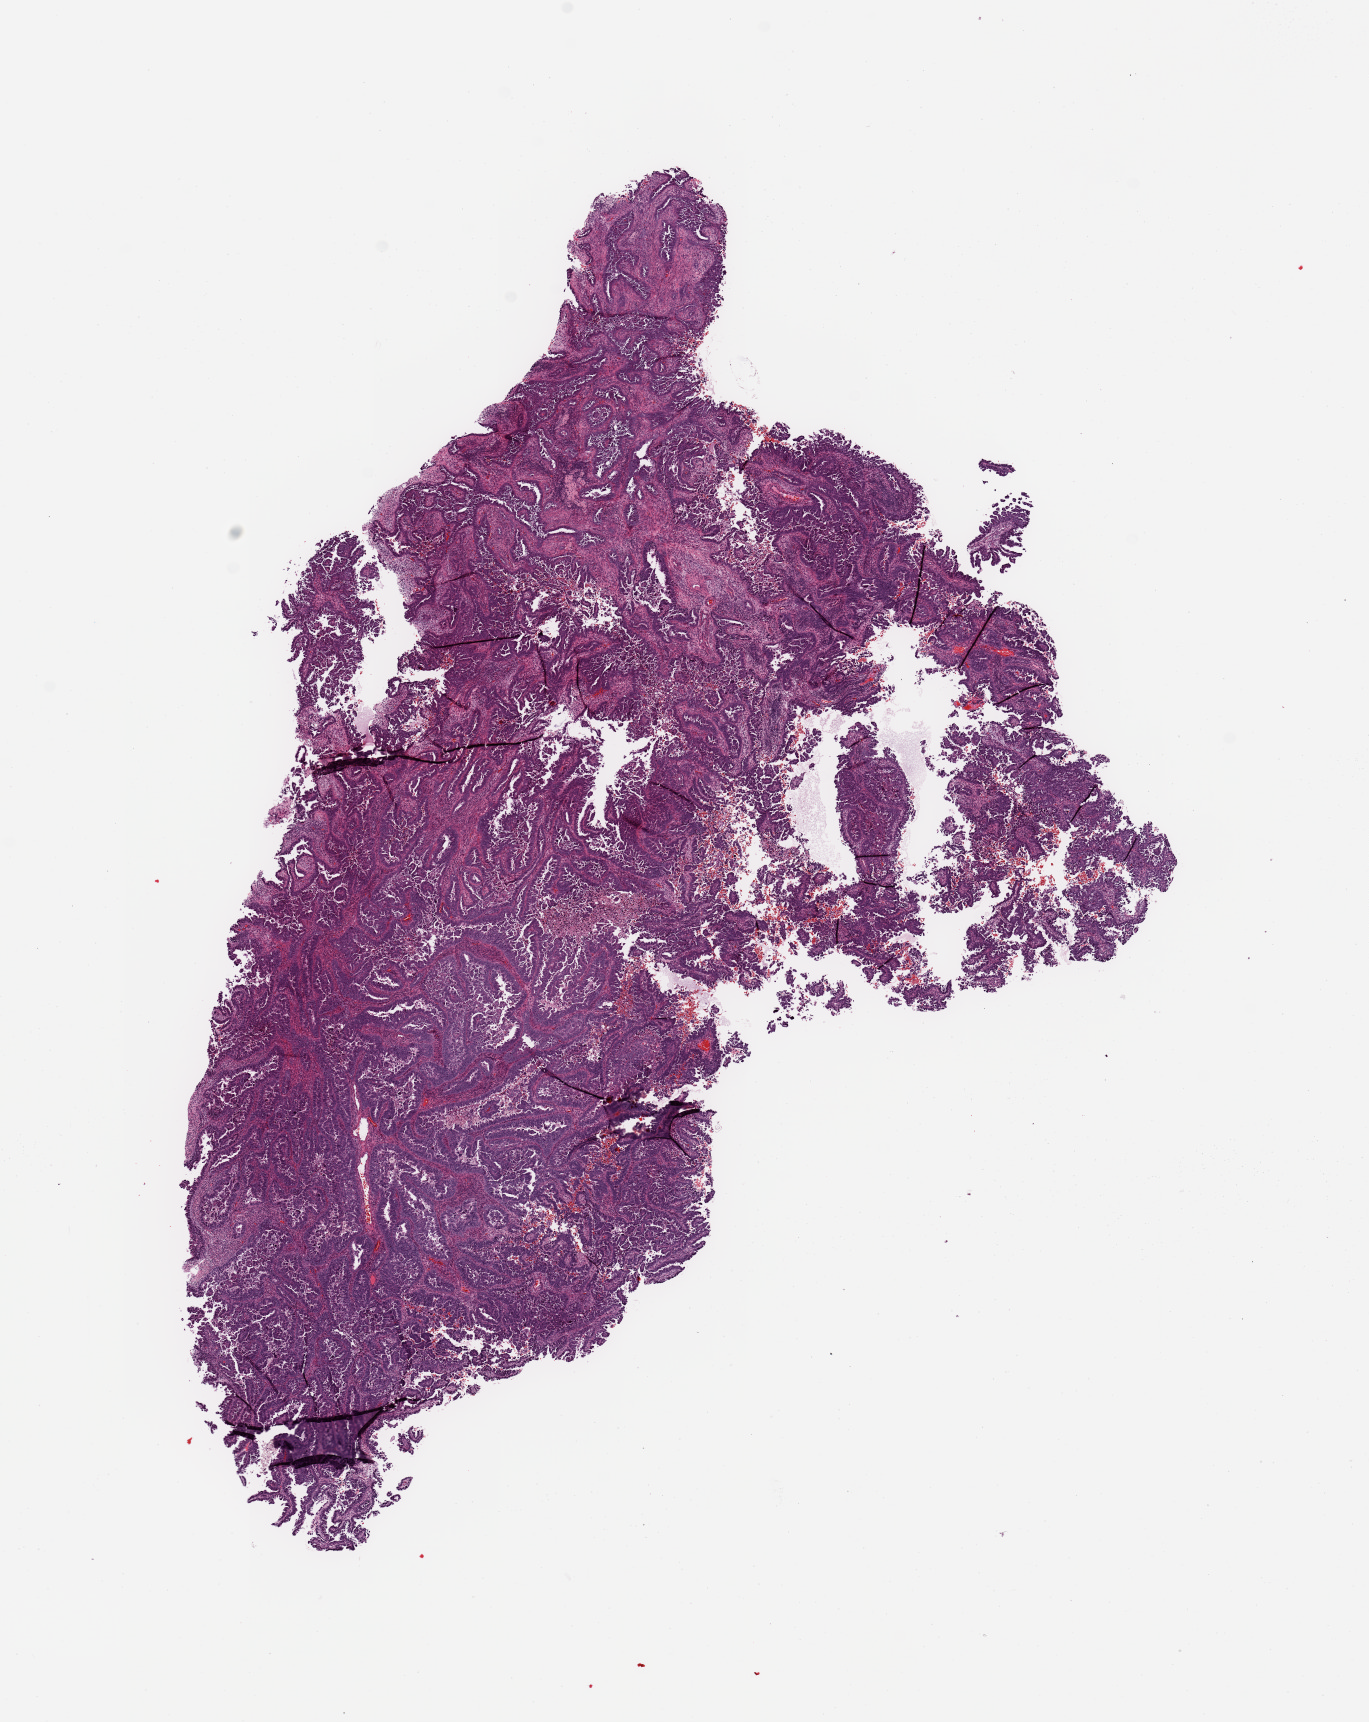
Digitized Hematoxylin and eosin (H&E) stained tissue section (whole slide), a low-resolution overview of the entire scanned area, about 10.8 x 13.6 mm; tumour tissue sample, sampled site: uterus. 83-year-old female patient. Composition of this section per pathologist review: tumour nuclei 90%, necrosis 5%.
AJCC pathologic stage: III. Histologic diagnosis: Endometrioid adenocarcinoma, NOS.